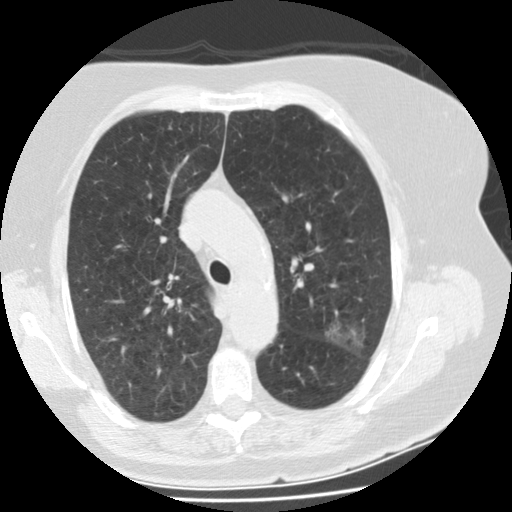
Low-dose screening chest CT, one axial slice. Position 109 of 151 along the scan axis. One of 2 acquisitions stored at this slice position. Lung window (W 1500 / L -600 HU). 512 × 512 image matrix, field of view 321 × 321 mm.
Annotated regions visible in this slice (expert manual segmentation):
- lesion 1 (tumor, upper lobe of left lung): bounding box (x1, y1, x2, y2) in pixels: (324, 320, 370, 354)